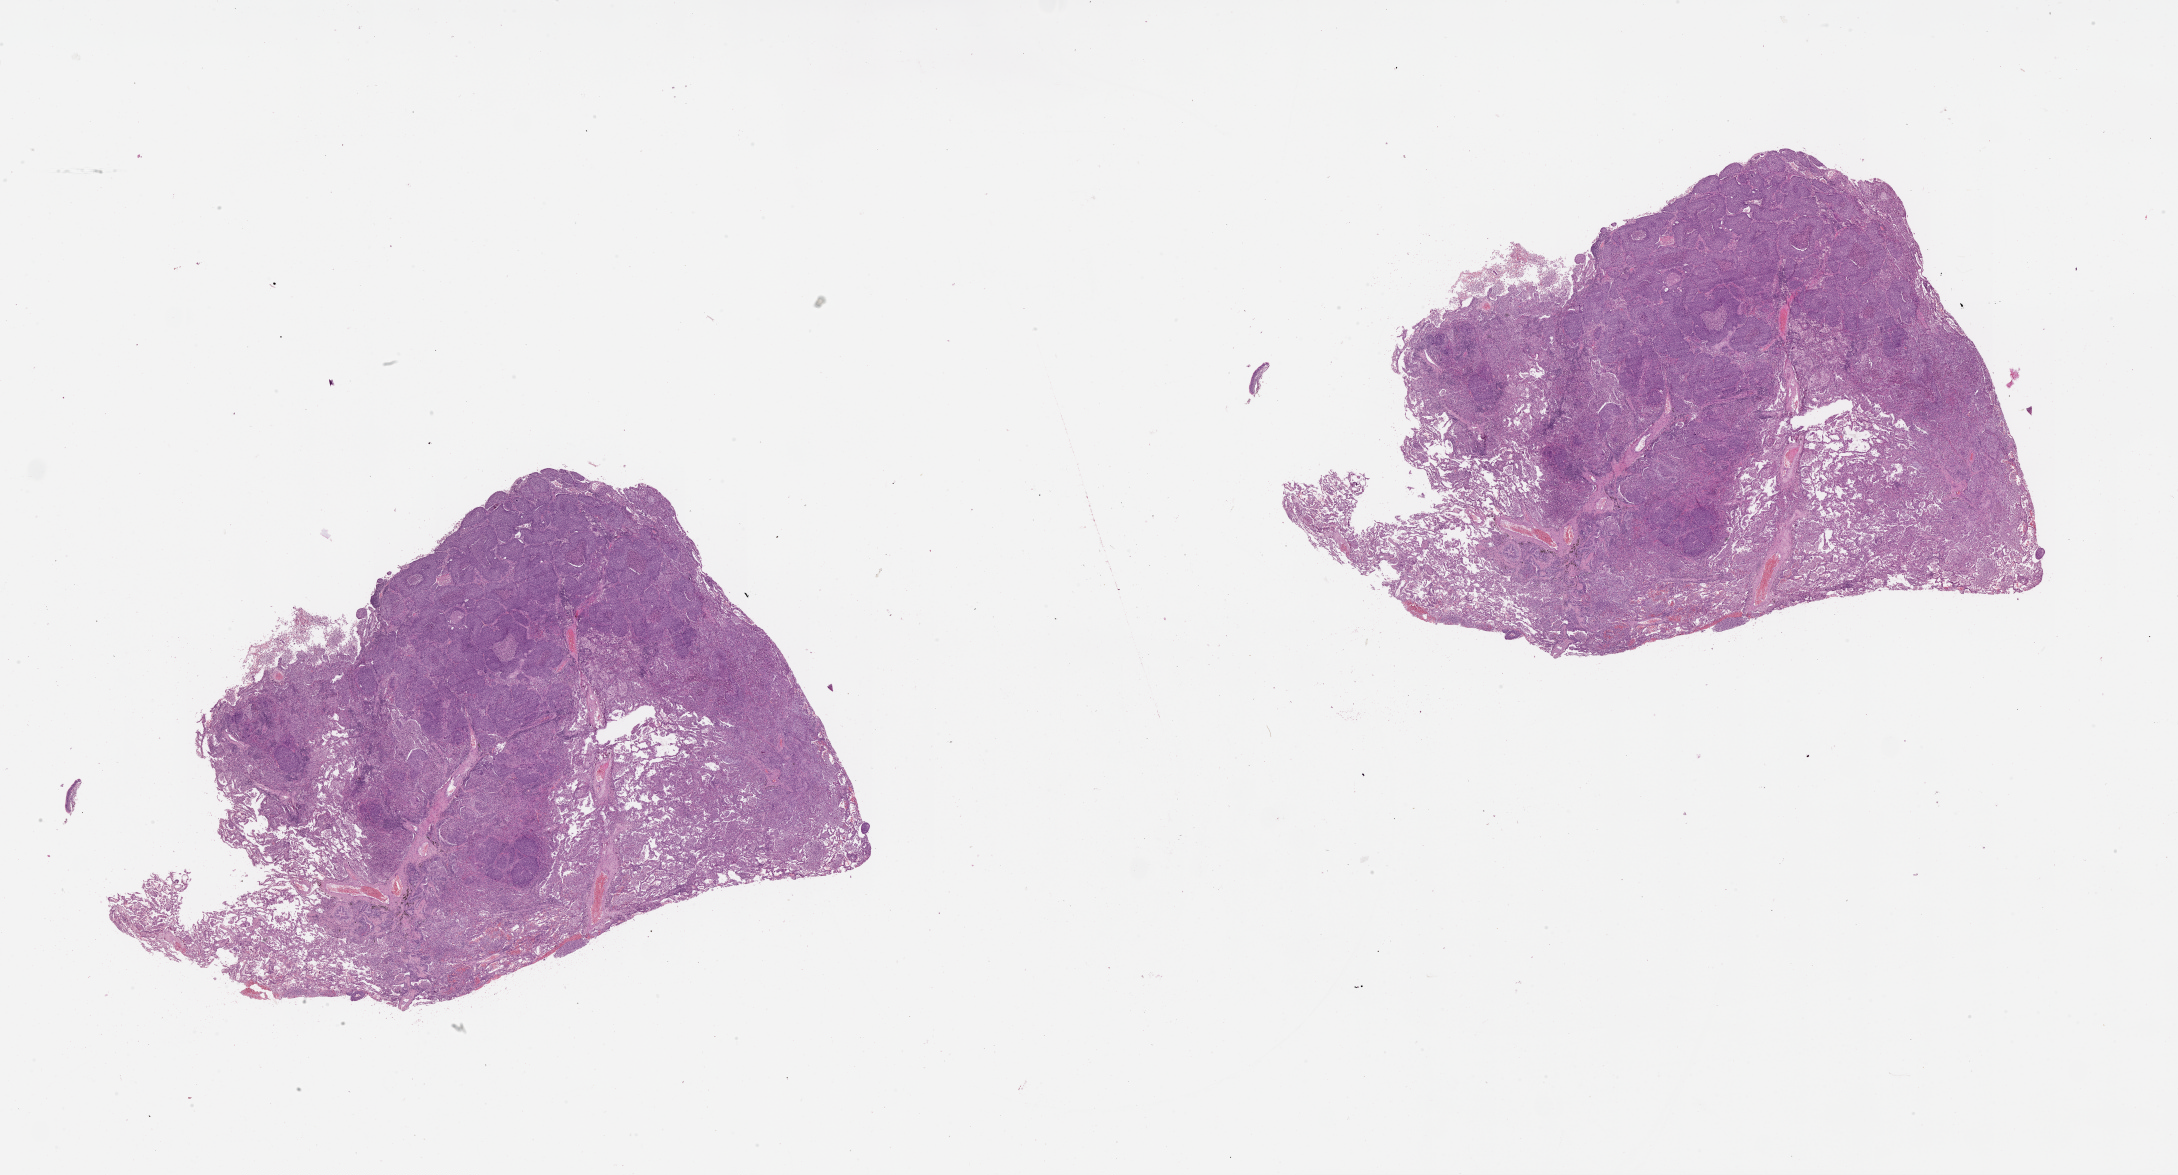
Digitized Hematoxylin and eosin (H&E) stained tissue section (whole slide), low-resolution overview of the scanned area, about 35.1 x 18.9 mm. Tumour tissue sample, lung. 63-year-old male patient.
• patient diagnosis (cohort enrolment): squamous cell carcinoma (lung)